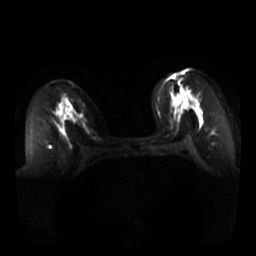
Breast MRI, one axial slice. Position 20 of 44 along the scan axis. Diffusion-weighted series; image 2 of 4 stored at this slice position (different b-values; order by instance number). 3 T. 5 mm slice thickness. 256 × 256 image matrix. Female patient.
Outlined on this slice (manually delineated by an expert):
- tumour on diffusion-weighted imaging: bounding box (x1, y1, x2, y2) in pixels: (175, 93, 189, 107)